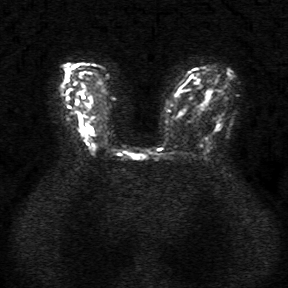
Breast MRI, one axial slice. Position 19 of 34 along the scan axis. Diffusion-weighted series; image 2 of 4 stored at this slice position (different b-values; order by instance number). 1.5 T. 5 mm slice thickness. 288 × 288 image matrix, field of view 340 × 340 mm. Female patient.
Structures marked on this image (expert manual segmentation):
- tumour on diffusion-weighted imaging: bounding box (x1, y1, x2, y2) in pixels: (90, 127, 93, 132)